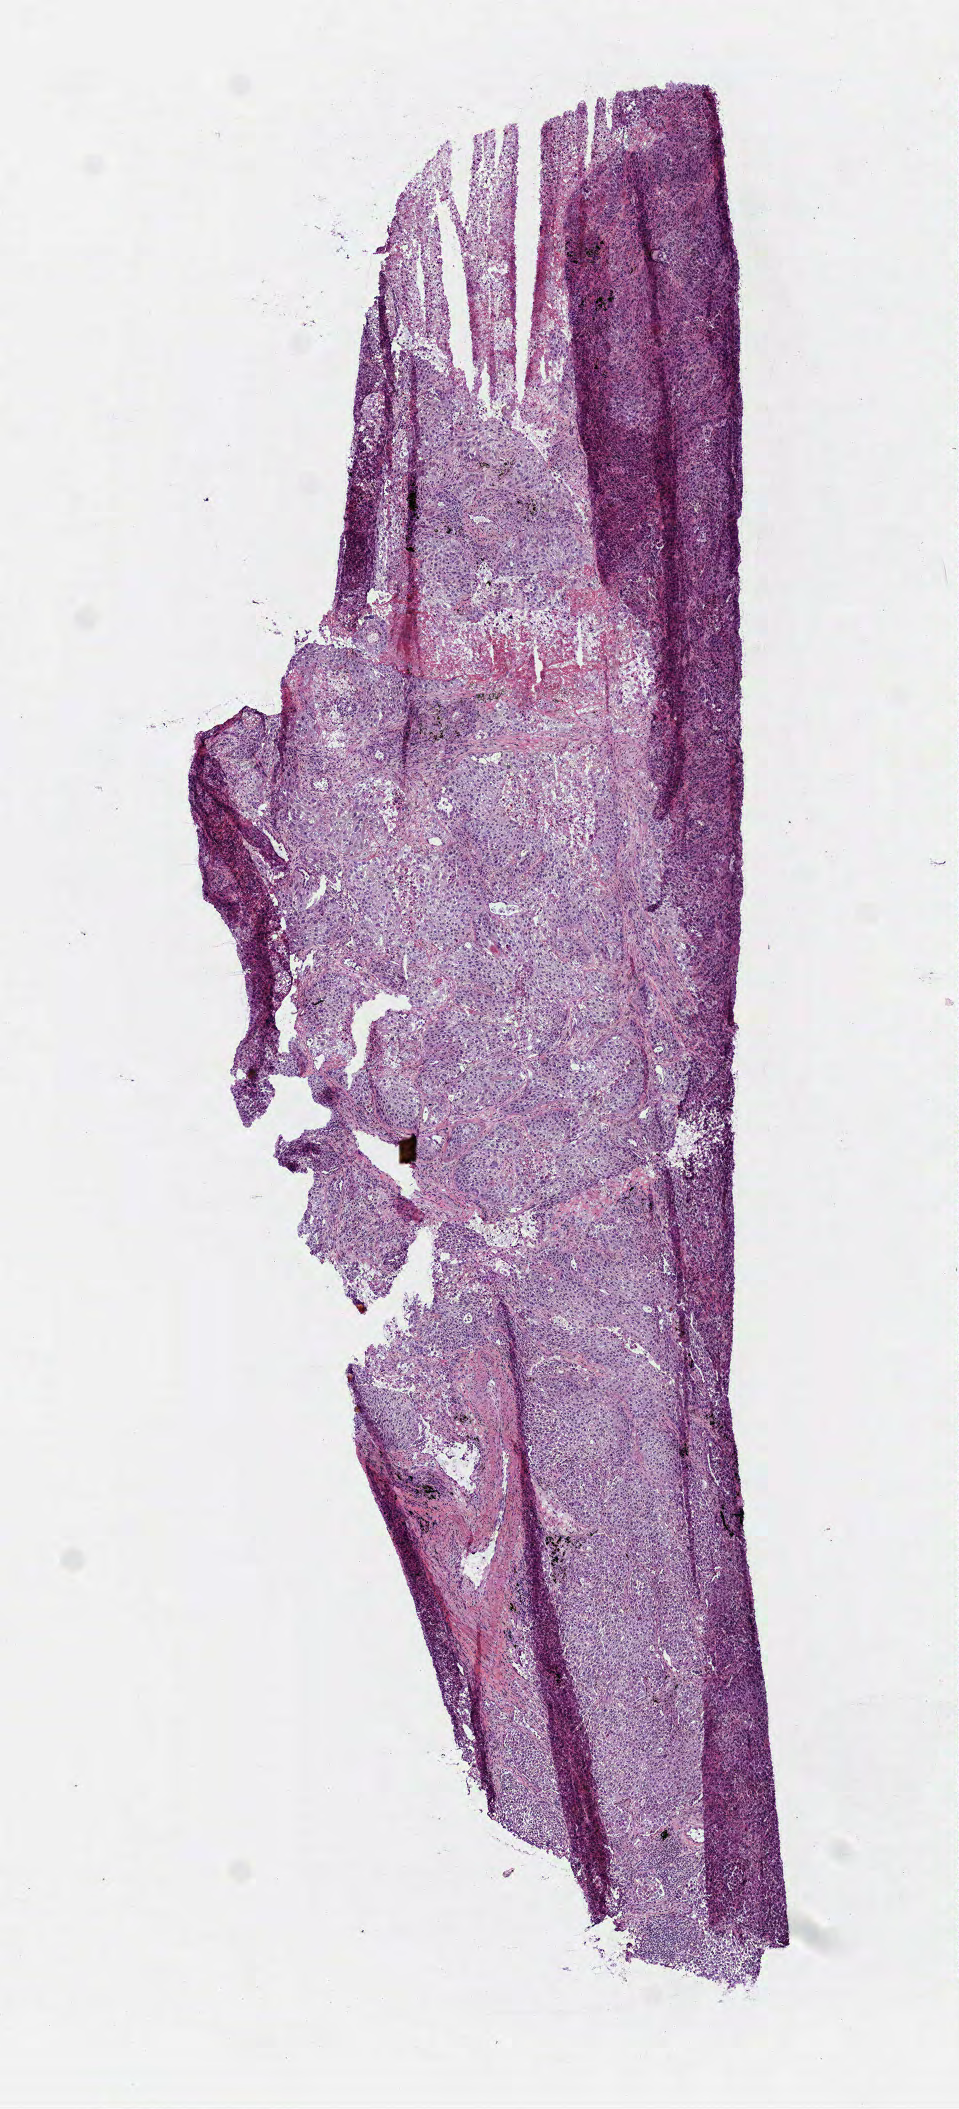
H&E-stained whole-slide image — a low-resolution overview of the entire scanned area, about 3.9 x 8.5 mm (slide scanned at 40x), frozen section, primary tumour sample from the lung. Patient sex: male. Composition of this section per pathologist review: tumour cells 80%, tumour nuclei 80%, normal cells 0%, stromal cells 6%, necrosis 14%. Infiltration values recorded for this section: lymphocyte infiltration 5%, monocyte infiltration 1%, neutrophil infiltration 2%.
- diagnosis: Squamous cell carcinoma, NOS
- AJCC pathologic stage: IA (6th edition)
- laterality: right